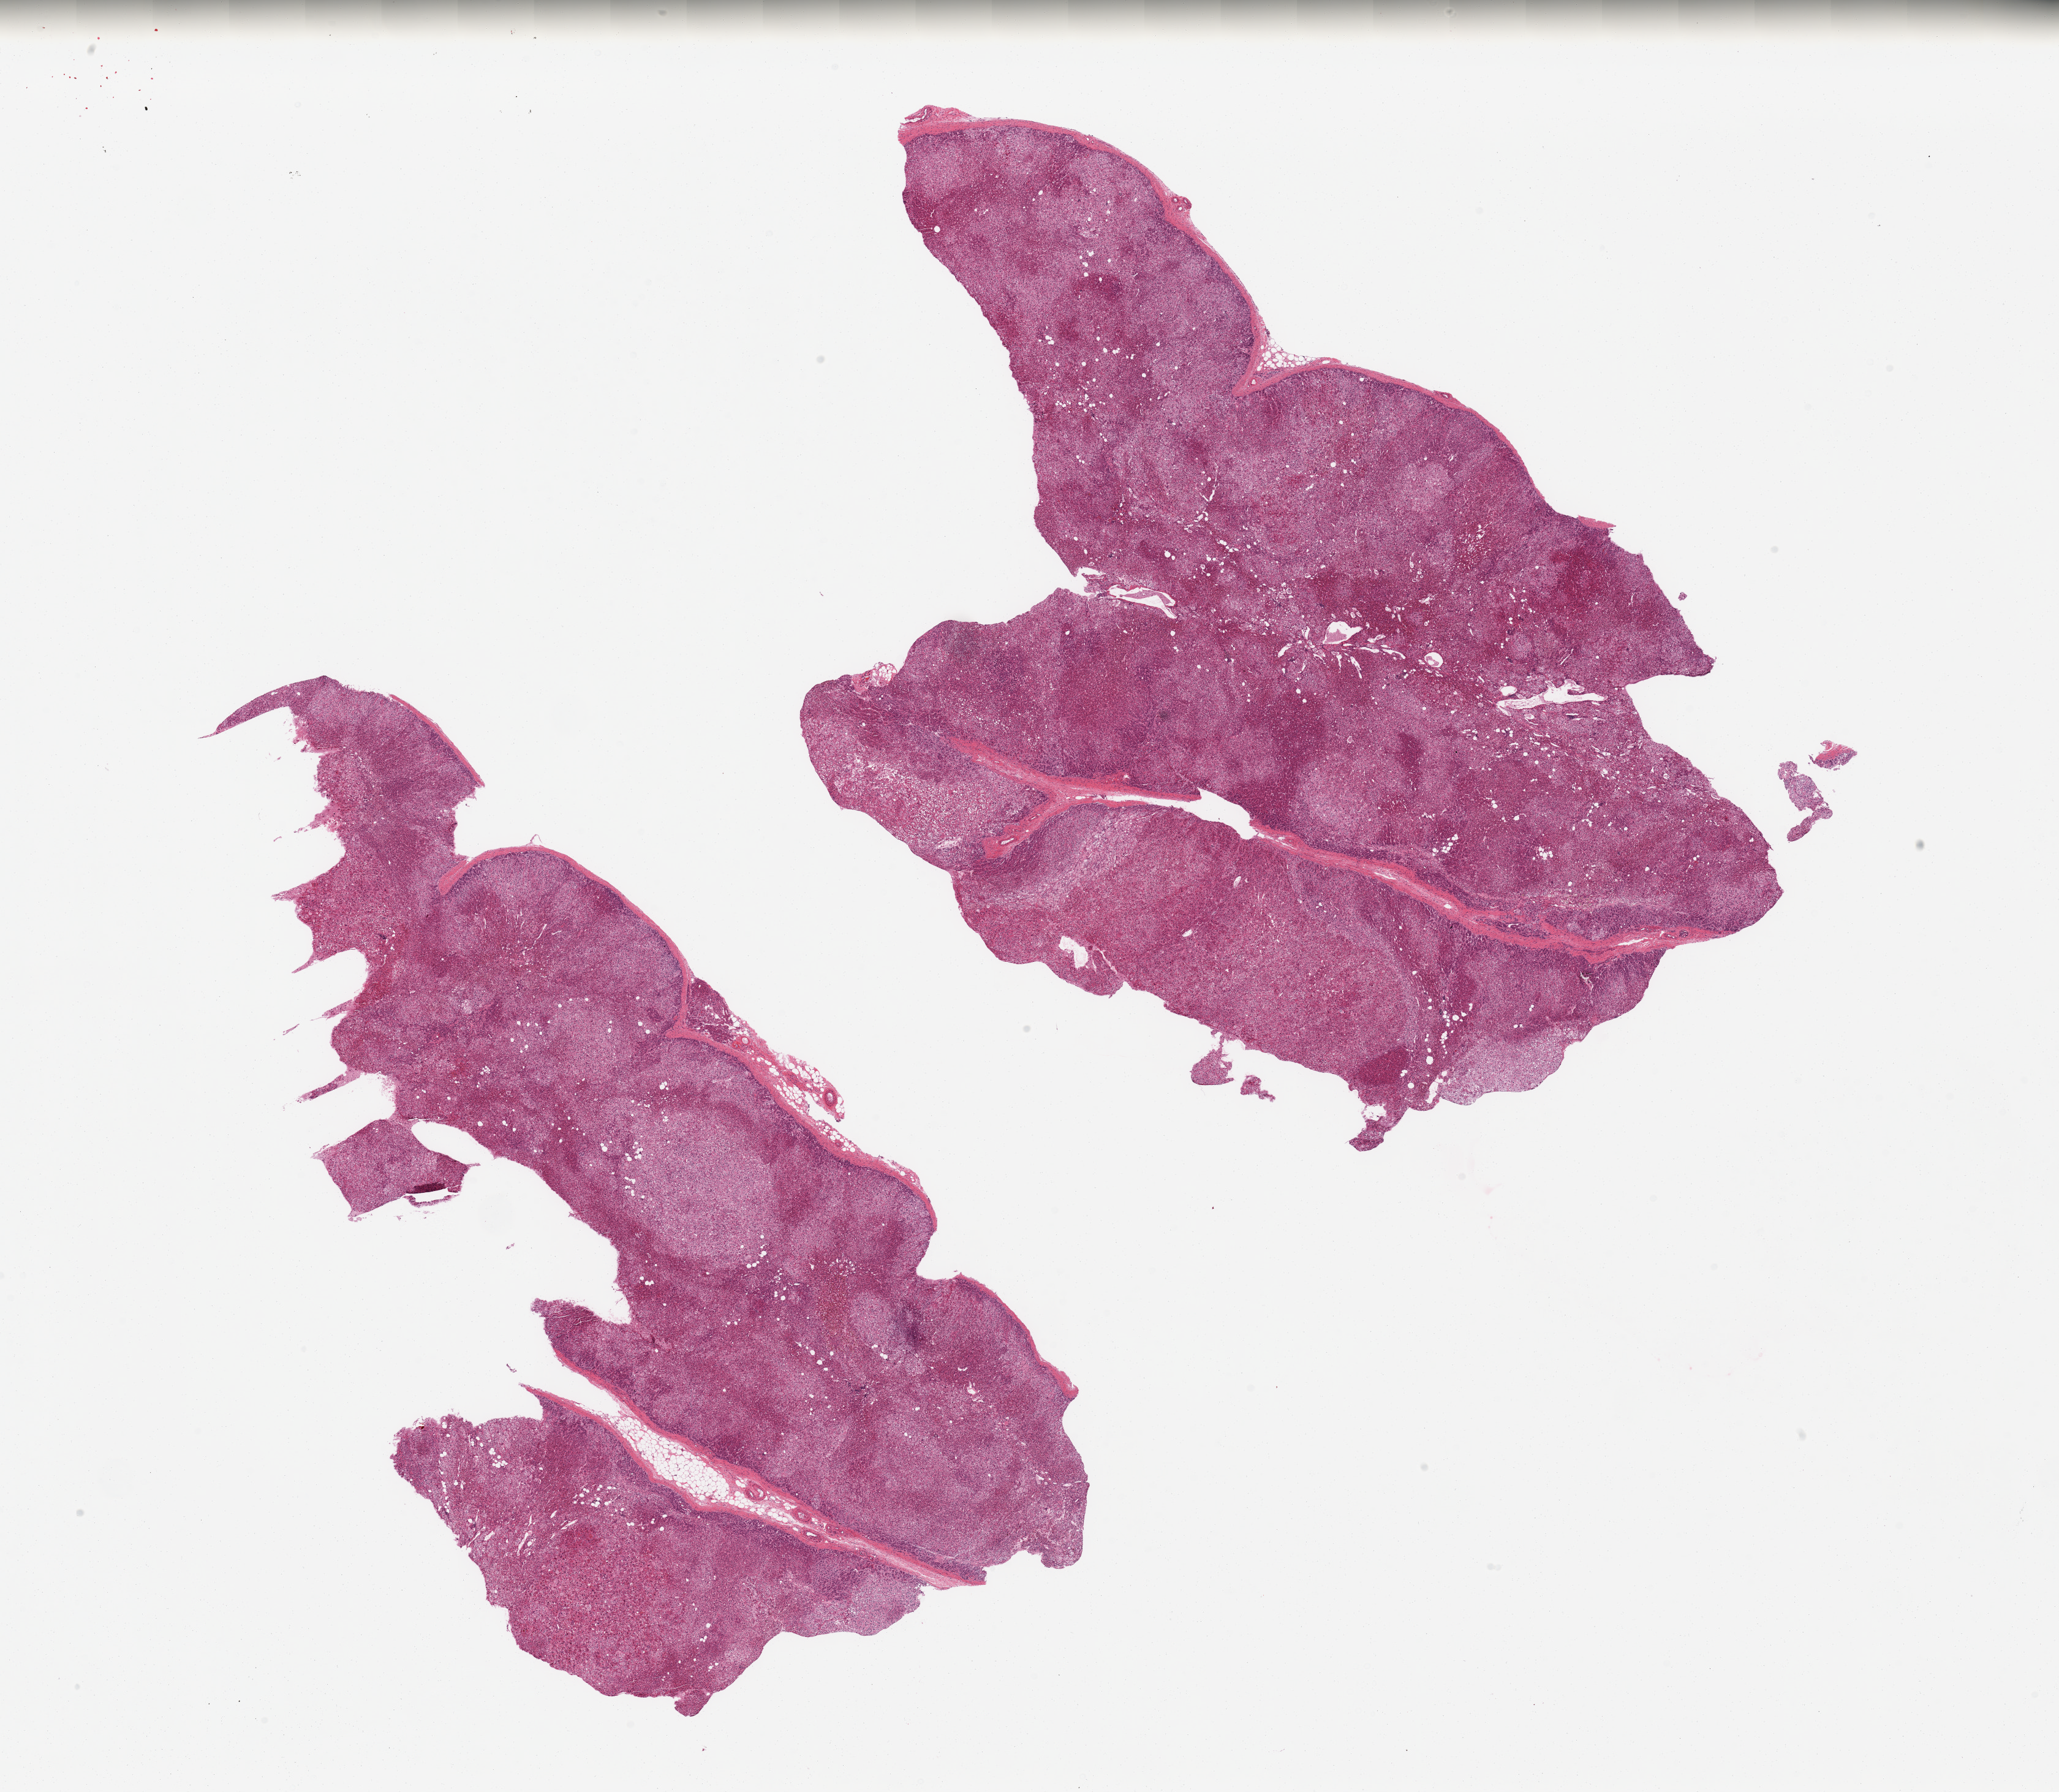
Whole-slide image, H&E stain, brightfield, low-resolution overview of the scanned area, about 26.6 x 23.1 mm (slide scanned at 20x), PAXgene-fixed paraffin-embedded (PFPE) section, target tissue: adrenal gland, donor tissue sample. Male donor.
• review note (as recorded): 2 pieces, unusually well preserved, all cortex, minimal fat